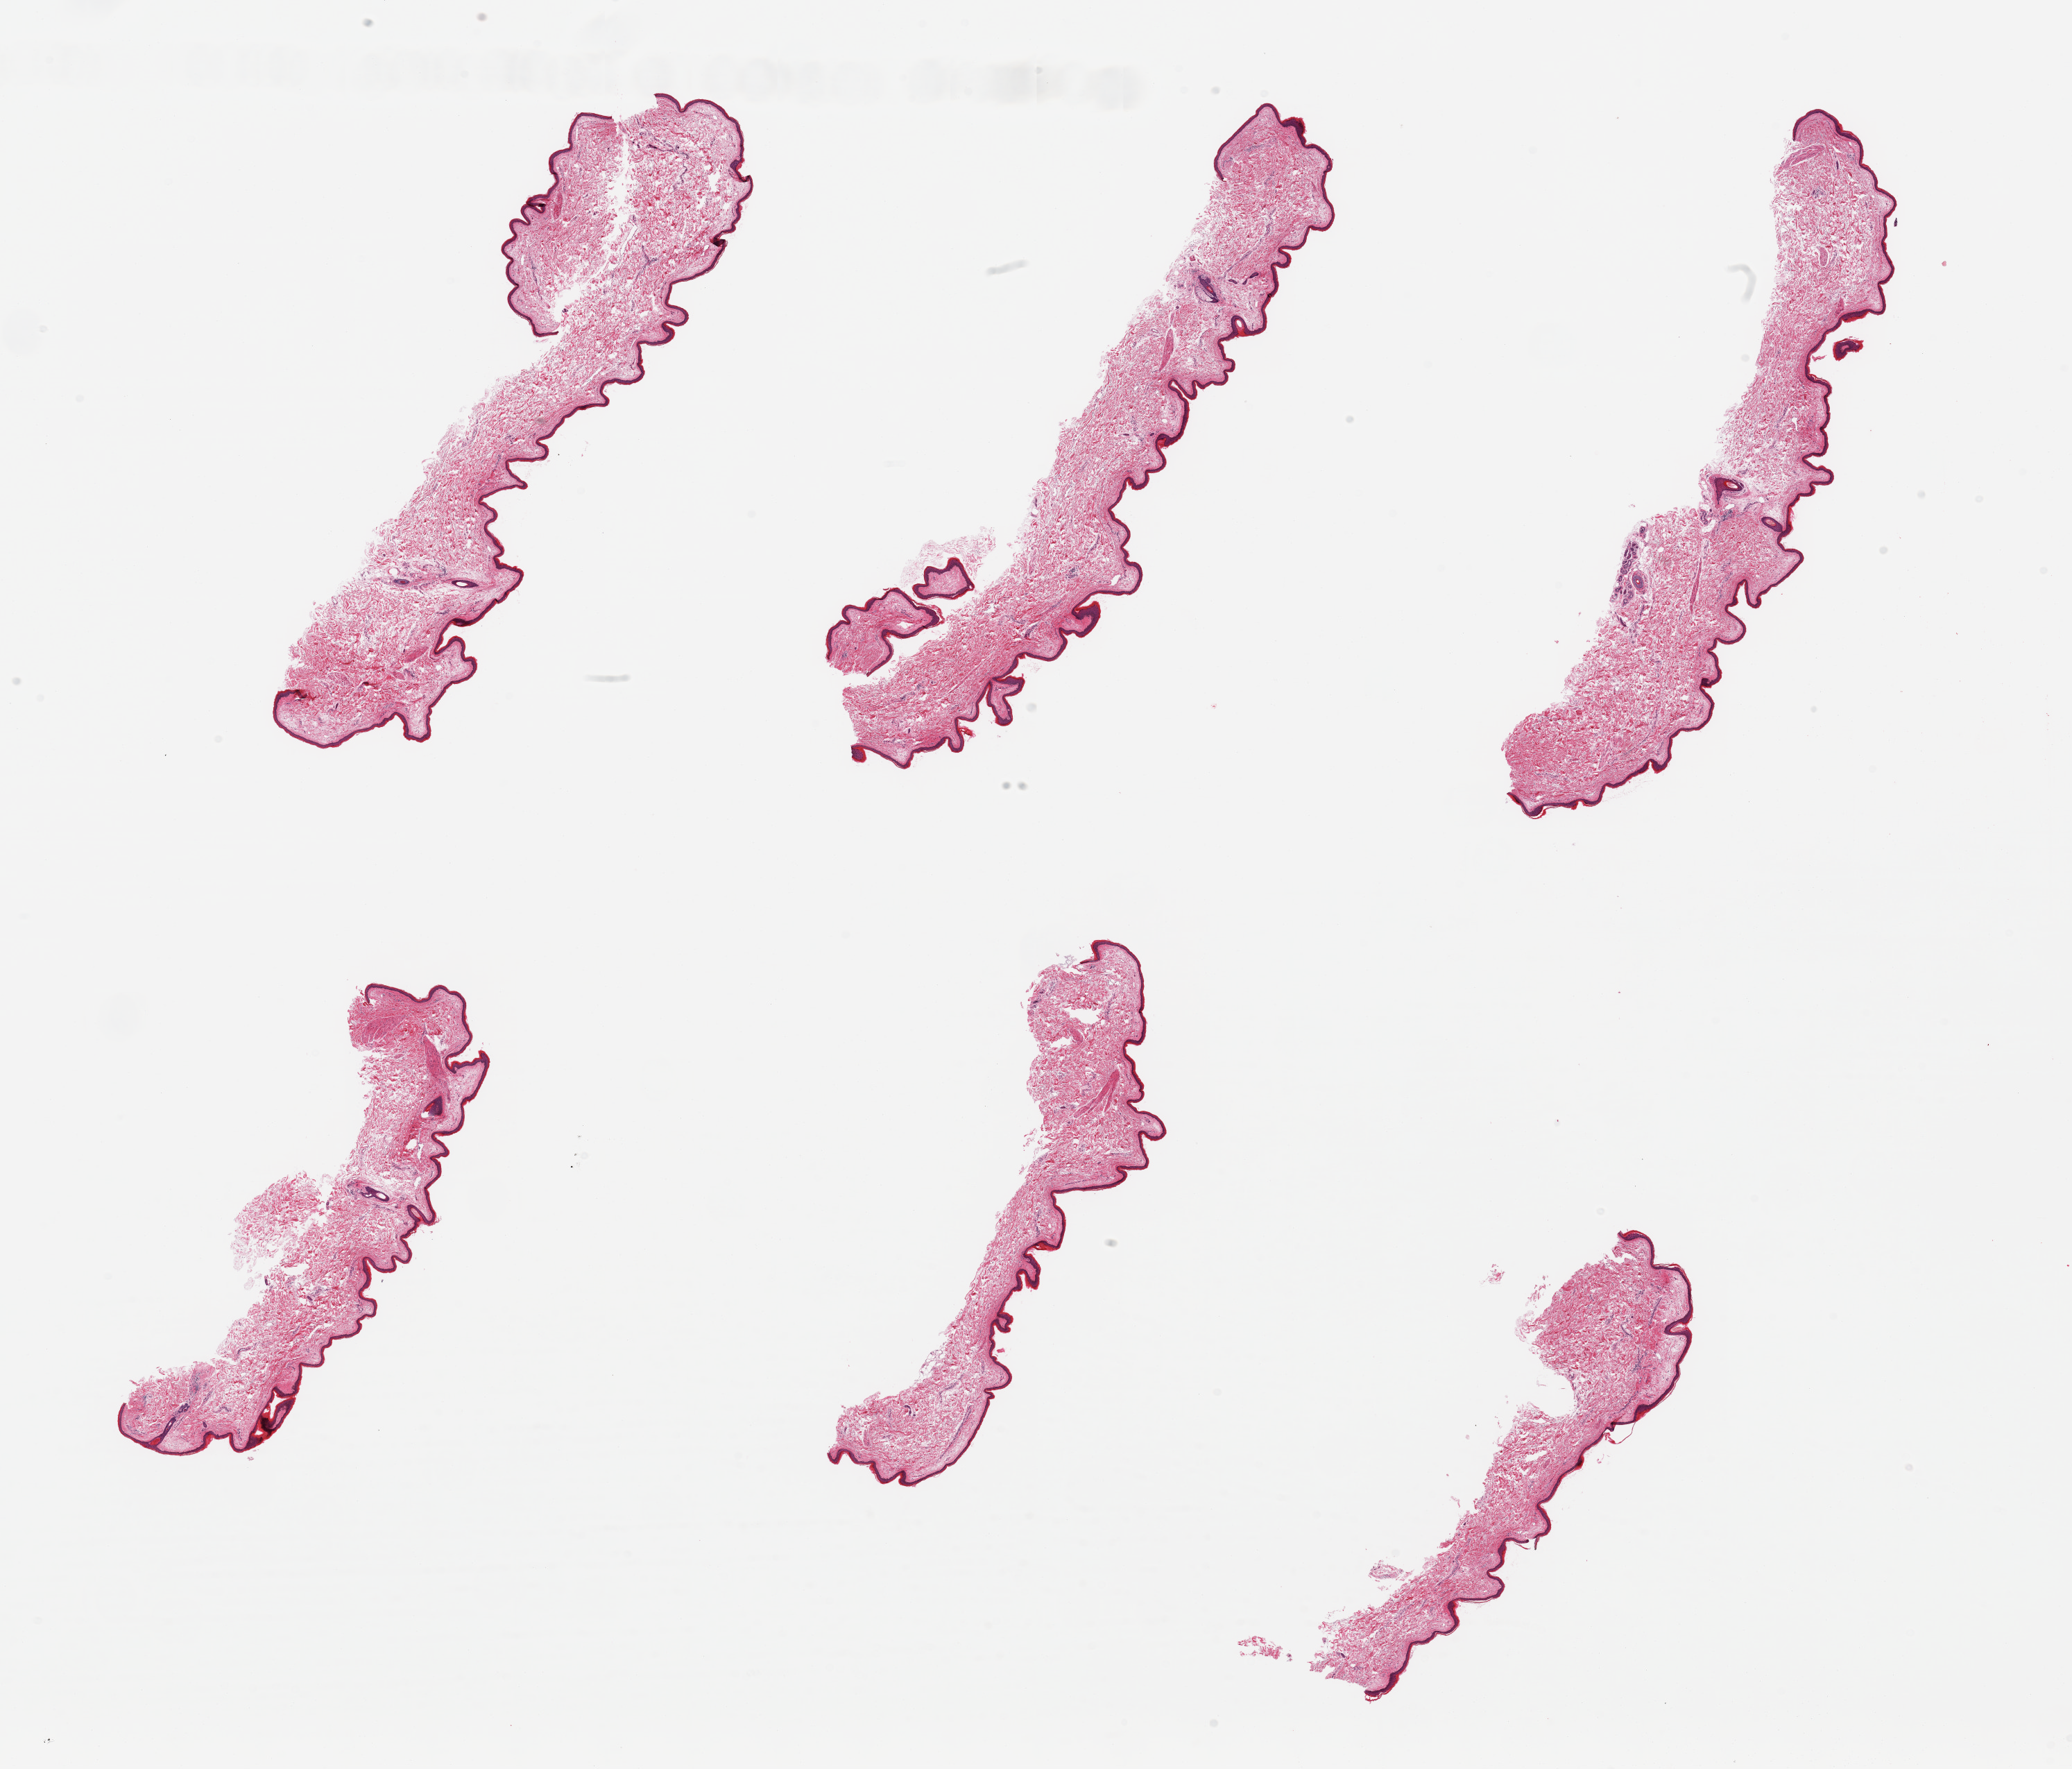
Whole-slide image, H&E stain — shown as a low-resolution overview of the whole scanned area (about 23.6 x 20.2 mm). PAXgene-fixed paraffin-embedded (PFPE) section. Section of skin of lower leg (target tissue). Tissue donor sample. Donor sex: male.
* pathologist's review note for this sample: 6 pieces; essentially well trimmed; epidermis ~35 microns